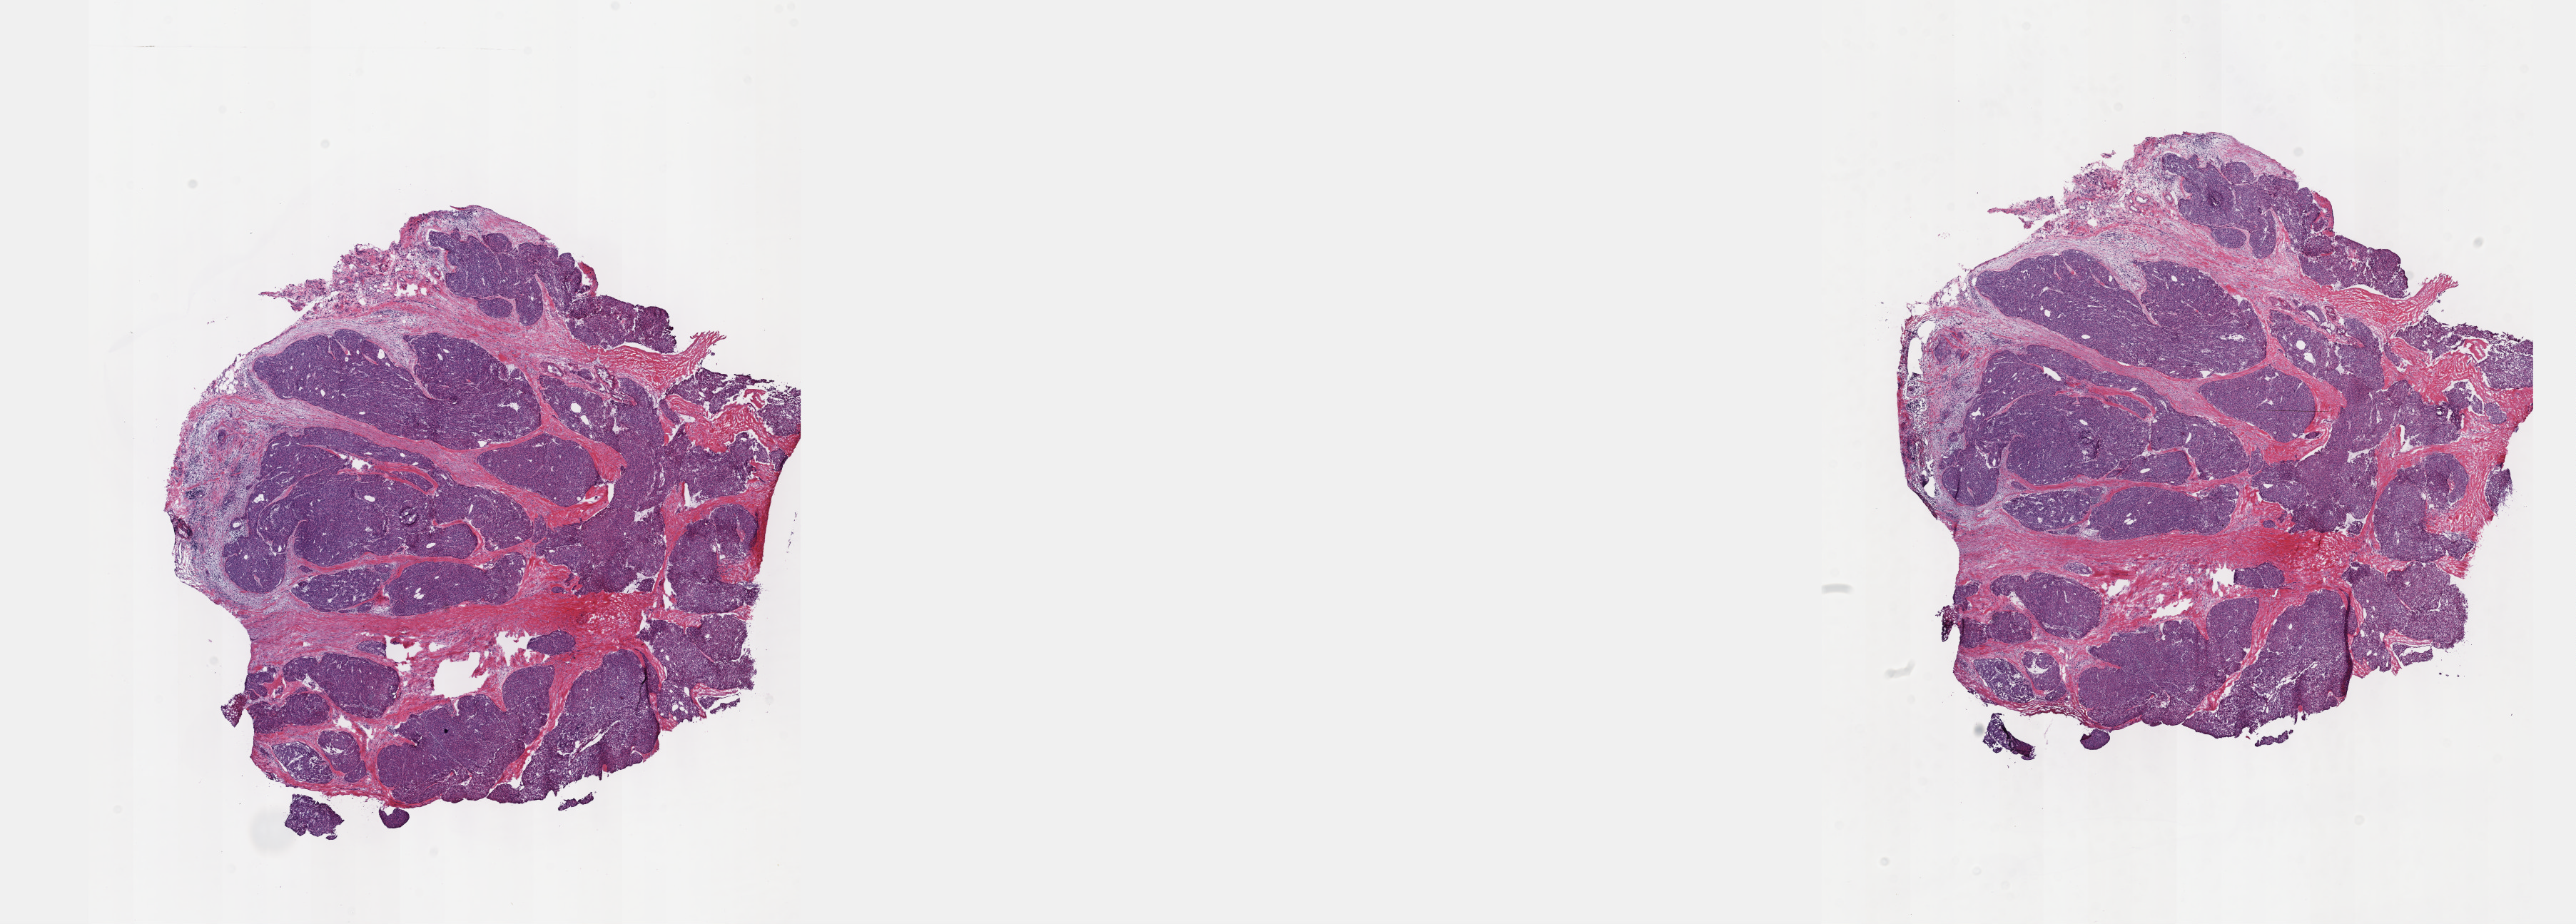
Whole-slide histology image, H&E-stained, a low-resolution overview of the entire scanned area, about 29.2 x 10.5 mm, frozen section from the top of the tissue portion, primary tumour sample from the thymus. Patient: female, age at initial diagnosis 72 years. Pathologist review of this section (percent, as recorded): tumour cells 60%, tumour nuclei 70%, normal cells 0%, stromal cells 40%, necrosis 0%. Inflammatory infiltration, as recorded: lymphocyte infiltration 0%, monocyte infiltration 0%, neutrophil infiltration 0%.
Histologic diagnosis: Thymic carcinoma, NOS (anterior mediastinum).